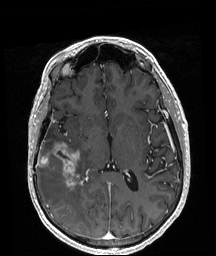
Brain MRI from a brain-tumour surgery series, one axial slice. Slice 102 of 208 in the series (ordered by position). T1-weighted post-contrast. 1 mm slice thickness. 216 × 256 image matrix, field of view 211 × 250 mm. From the clinical record (not read from this slice): histopathology: Astrocytoma; WHO grade: 4; IDH mutation: yes.
Annotated regions visible in this slice (manually delineated by an expert):
- tumour: bounding box [x1, y1, x2, y2] px = [38, 143, 79, 189]